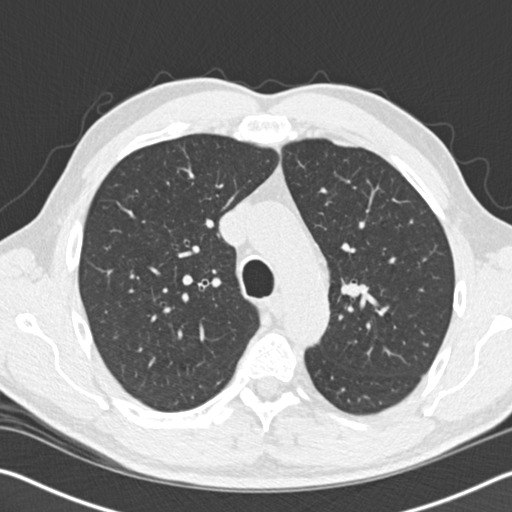
Chest CT (low-dose screening protocol), one axial image. First (baseline) screen. Lung window (W 1500 / L -600 HU). 2 mm slice thickness. Standard (soft-tissue) reconstruction kernel (B30f). 120 kVp. Slice 54 of 162 in the series. 512 × 512 image matrix. Male, age 61 years at enrolment.
• Expert-annotated lung lesion, bounding box <341,273,374,317> (left, top, right, bottom; pixels).
• The screening reader recorded 2 non-calcified nodules or masses ≥4 mm on this exam (right middle lobe, left upper lobe); which of them this box marks is not recorded.
• Lung cancer was diagnosed 183 days after this screen: small cell carcinoma, NOS, left upper lobe, stage IIIB (AJCC 6th edition), 100 mm at pathology.